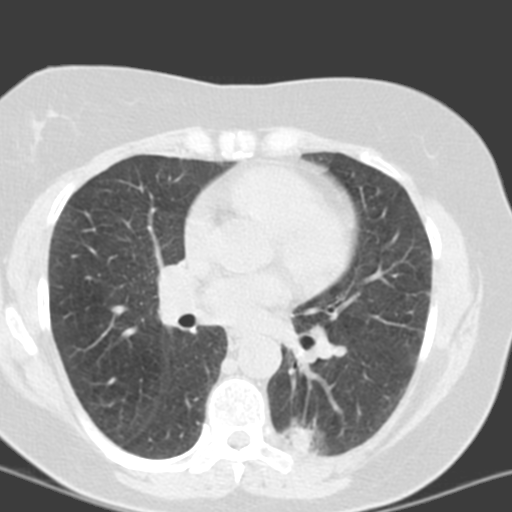
Low-dose screening chest CT, axial slice; third screening round (two years after baseline); lung window (W 1500 / L -600 HU); 3.2 mm slice thickness; standard (soft-tissue) reconstruction kernel (B); slice 66 of 150 in the series. Female participant, aged 55 years at enrolment. Current smoker at enrolment.
Expert-annotated lung lesion, box from (x=282, y=408) to (x=362, y=463) px. The screening reader recorded 6 non-calcified nodules or masses ≥4 mm on this exam (left lower lobe, left lower lobe, left upper lobe, lingula, lingula, right middle lobe); which of them this box marks is not recorded. Lung cancer was diagnosed 357 days after this screen: adenocarcinoma with mixed subtypes, left lower lobe, poorly differentiated (G3), stage IA (AJCC 6th edition), 21 mm at pathology.